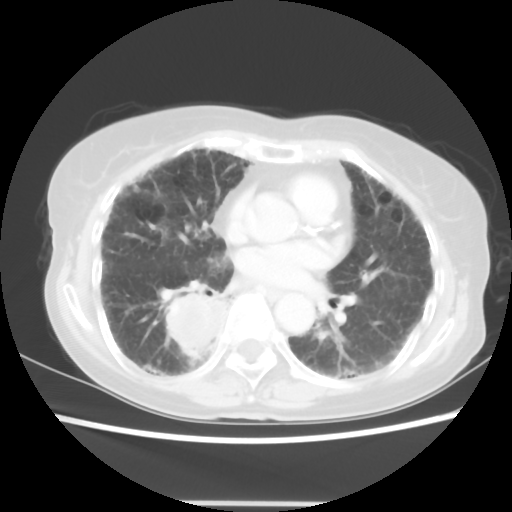
Chest CT, one axial slice. Slice 26 of 52 in the series (ordered by position). Reconstruction kernel STANDARD. Lung window (W 1500 / L -600 HU). 5 mm slice thickness. 512 × 512 image matrix. Female patient, age 71 years. Case-level facts recorded for this patient, not image findings: clinical TNM (as recorded): T3 N0 M0.
Outlined on this slice (bounding box drawn by a radiologist):
- lung tumour (recorded histology: squamous cell carcinoma): bounding box (x1, y1, x2, y2) in pixels: (162, 292, 223, 364)